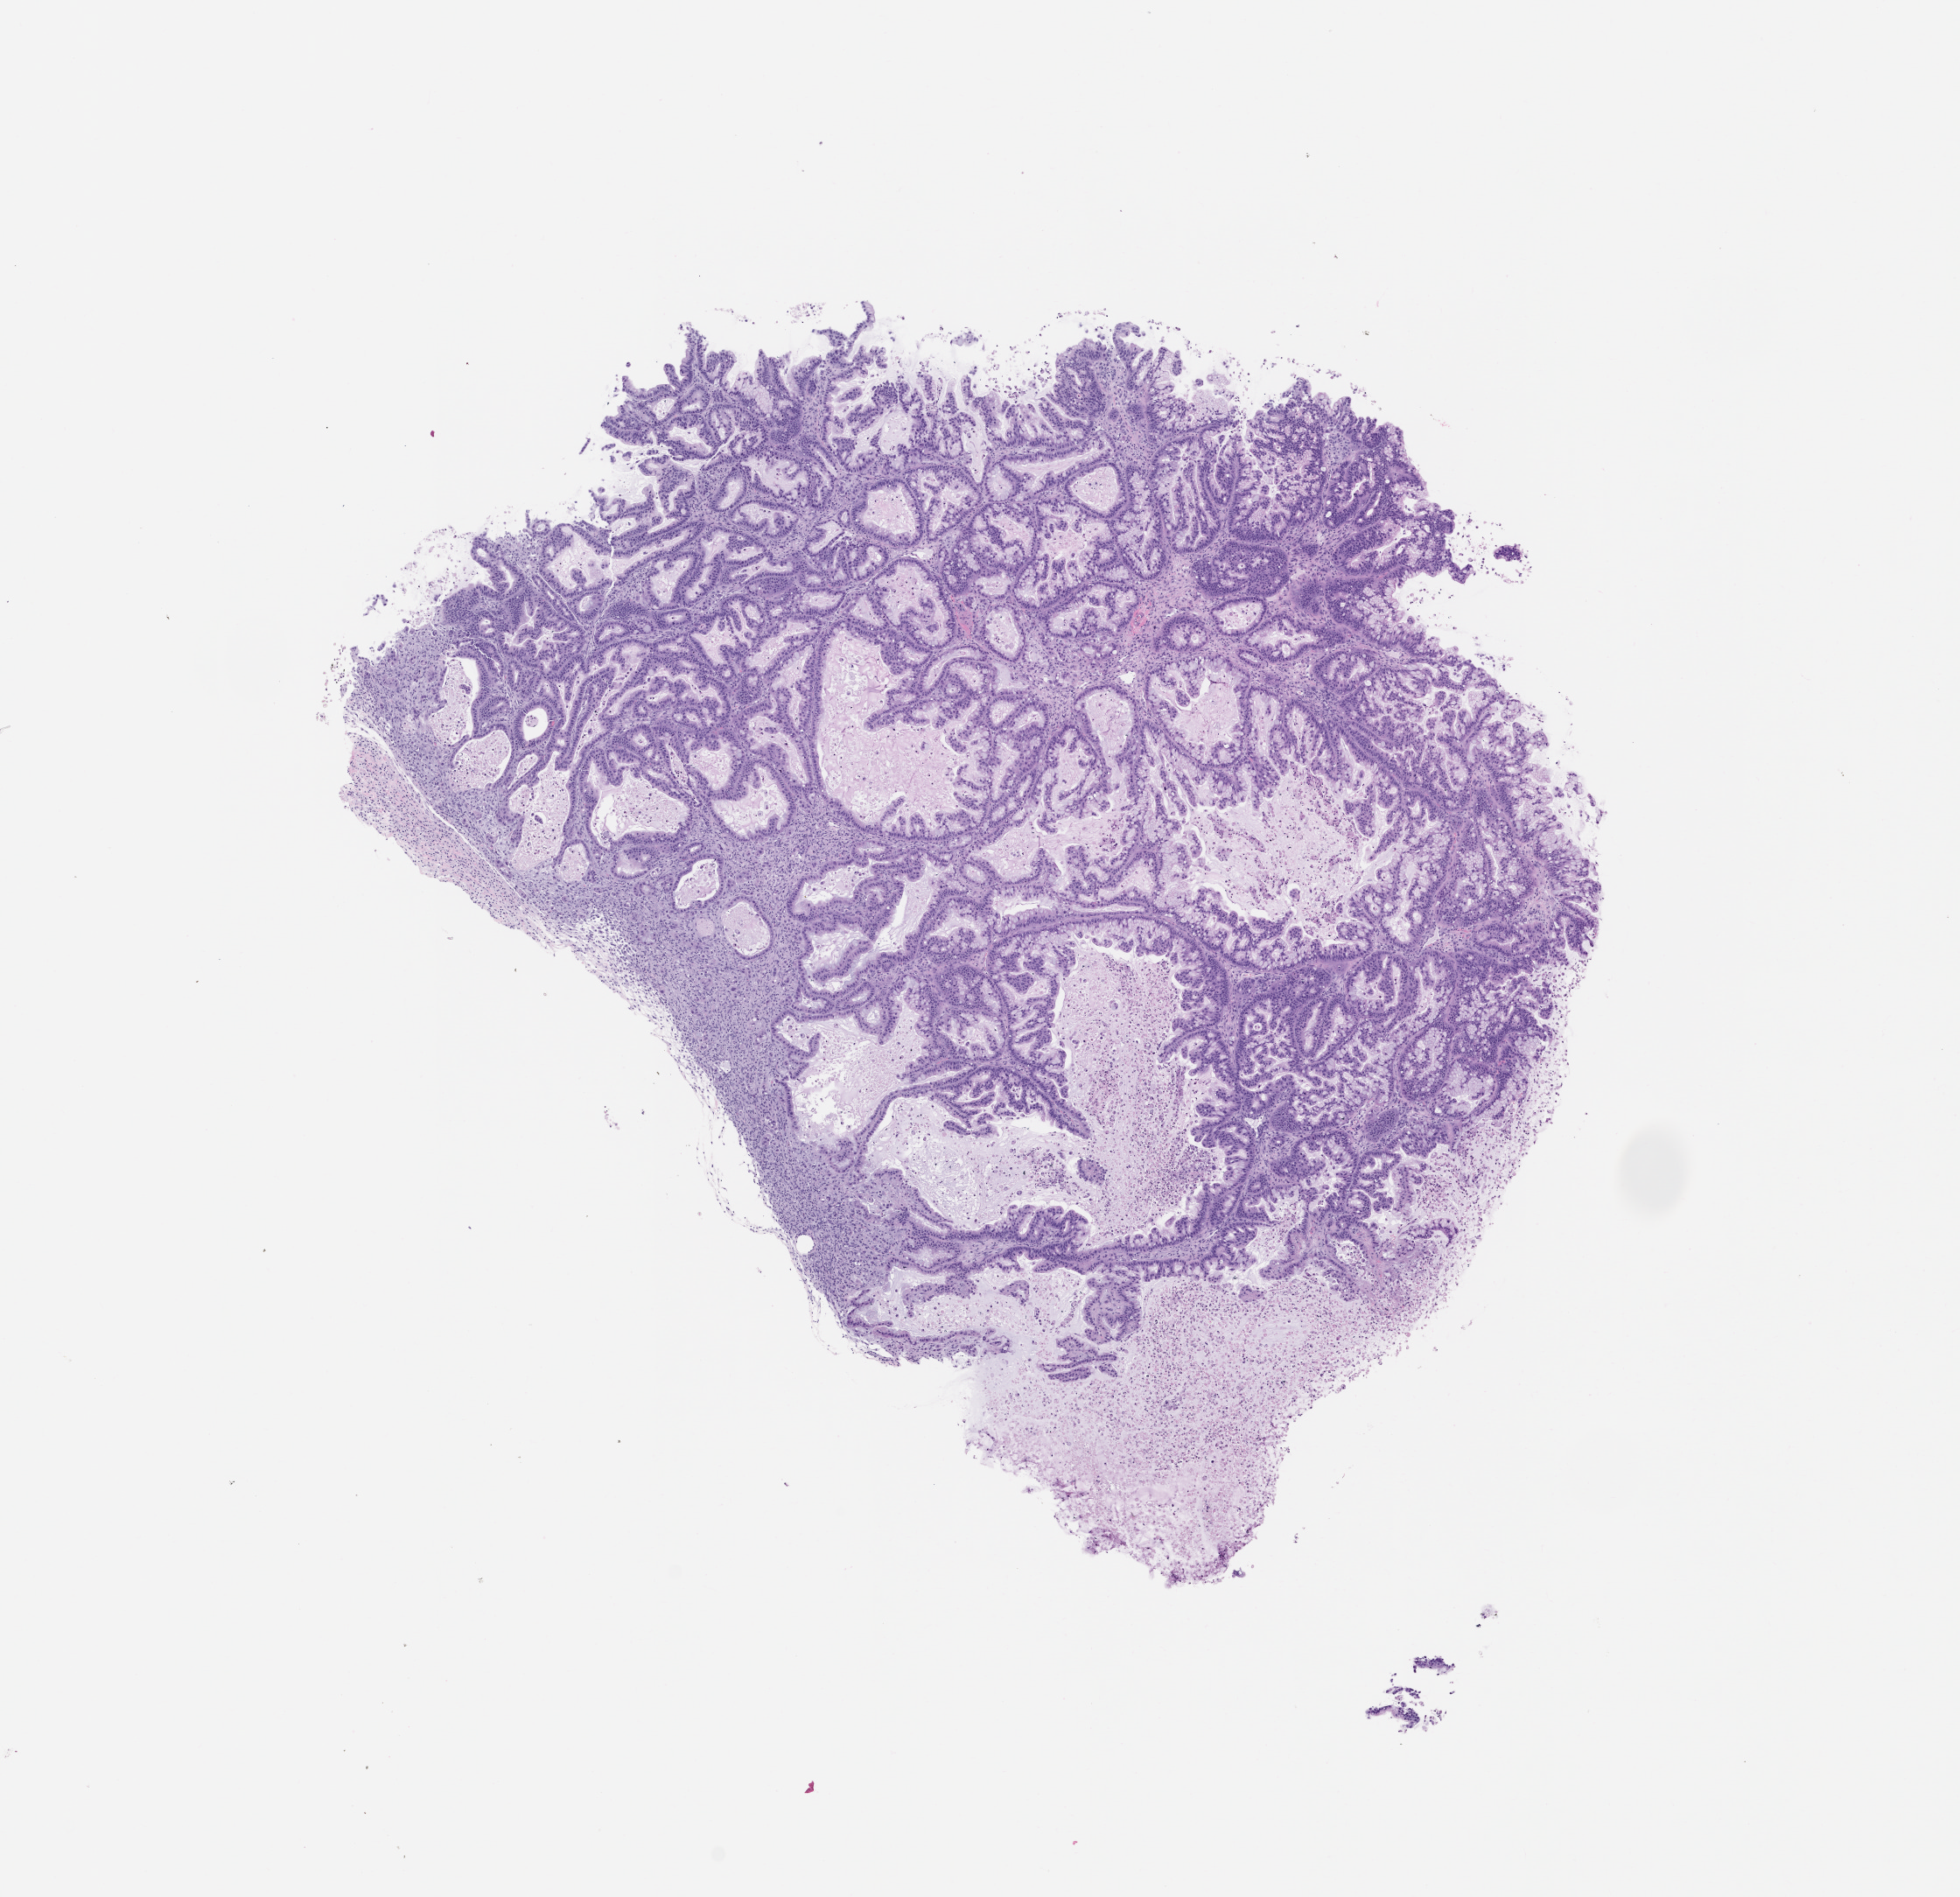
H&E whole-slide image of a patient-derived xenograft (PDX) tumor grown in a mouse, passage 1, whole scanned area (about 9.0 x 8.7 mm) shown as a low-resolution overview. Formalin-fixed, paraffin-embedded (FFPE) tissue. Tumor site category: pancreas.
Originating patient diagnosis: Pancreatic Adenocarcinoma.